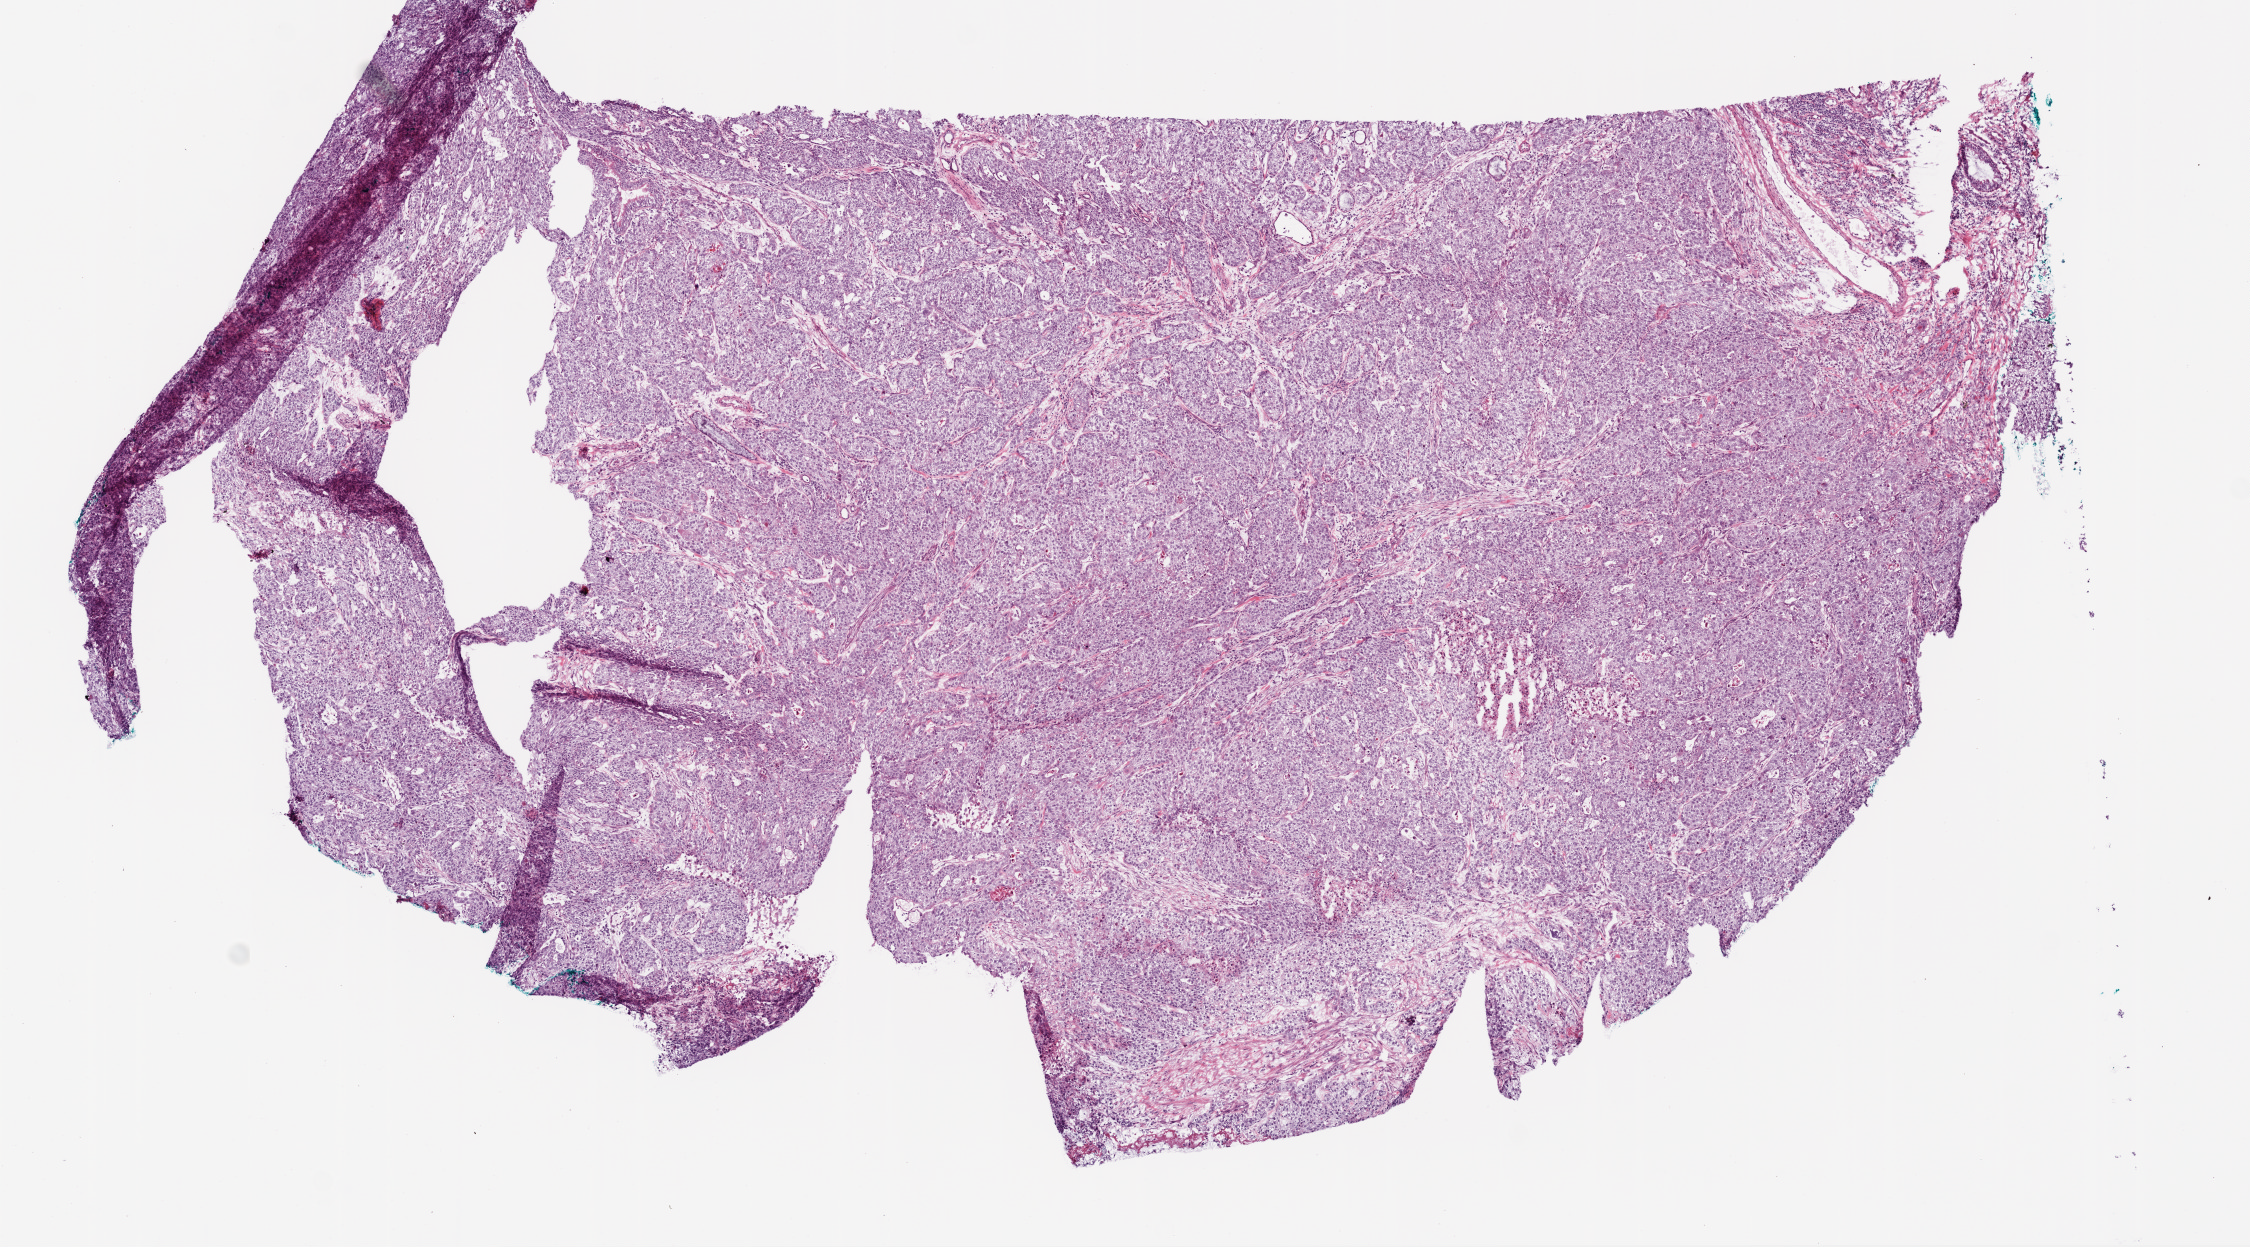
Whole-slide histology image, H&E-stained, shown as a low-resolution overview of the whole scanned area (about 9.0 x 5.0 mm); frozen section; sample: primary tumour, lung. Patient: male, age at initial diagnosis 58 years. Slide review estimates, as recorded: tumour cells 89%, tumour nuclei 90%, normal cells 0%, stromal cells 10%, necrosis 1%.
* AJCC pathologic stage: IB
* histologic diagnosis: Squamous cell carcinoma, NOS